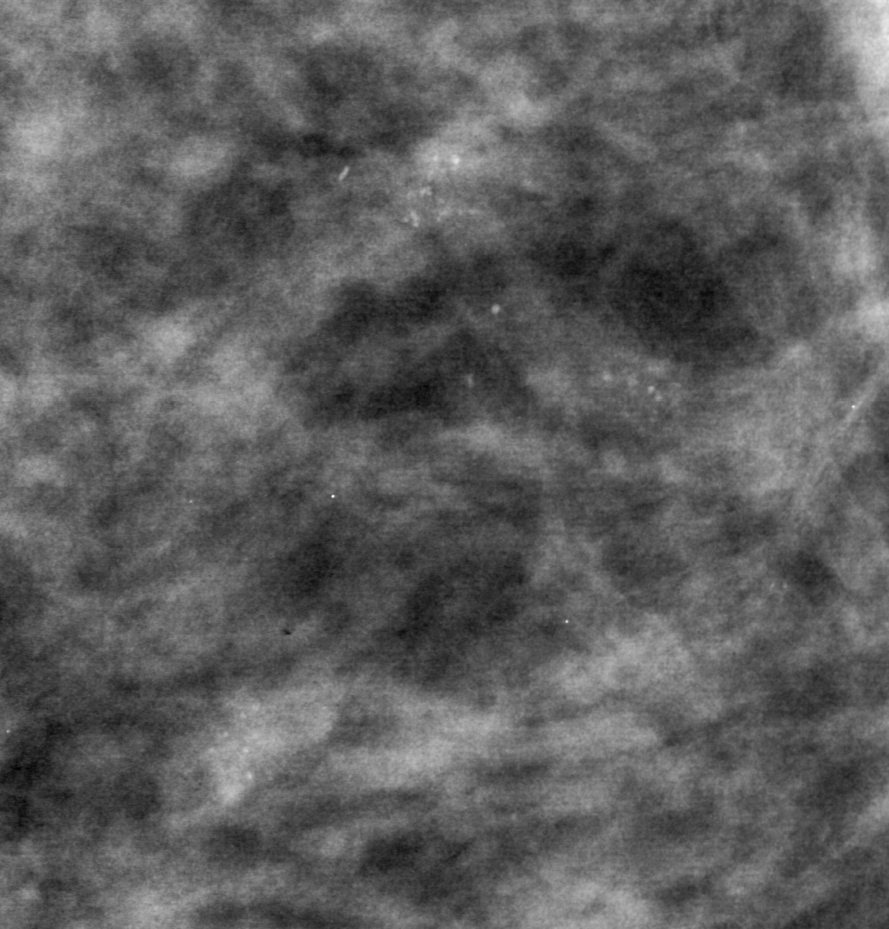
Region of interest cut from a scanned film mammogram (one marked finding), left breast, MLO view, BI-RADS breast density category 3 (scale 1–4).
- Finding: calcifications, morphology pleomorphic, distribution segmental; BI-RADS assessment category 4; subtlety rating 3 on a 1 (subtle) to 5 (obvious) scale; pathology result (as recorded, not read from the image): malignant.